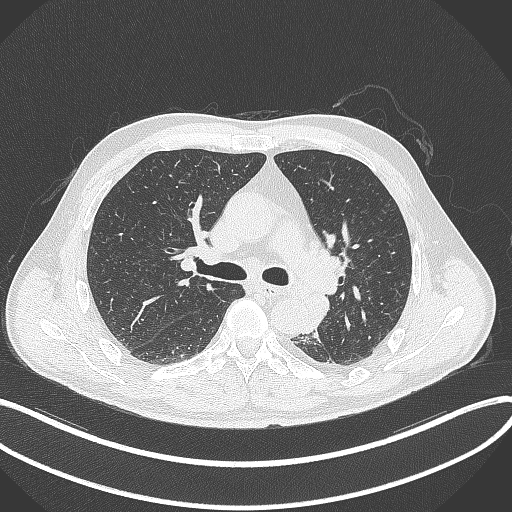
Chest CT, one axial slice. Position 216 of 329 along the scan axis. Reconstruction kernel B70f. 120 kVp. Lung window (W 1500 / L -600 HU). 512 × 512 image matrix, field of view 400 × 400 mm. Male patient, age 59 years. From the clinical record (not read from this slice): clinical TNM (as recorded): T2a N2 M0.
Structures marked on this image (rectangle marked by the reading radiologist):
- lung tumour (recorded histology: squamous cell carcinoma): bounding box [x1, y1, x2, y2] px = [301, 291, 332, 336]